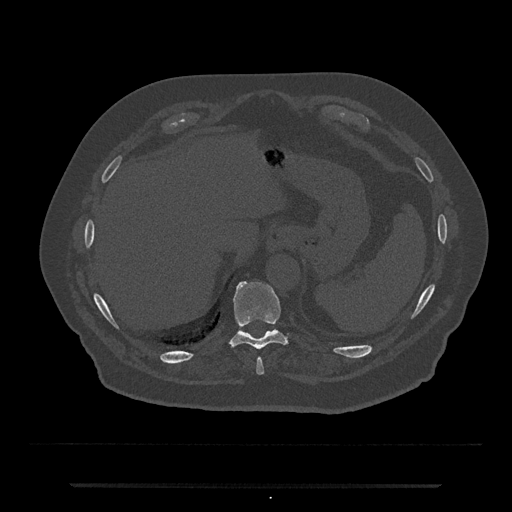
CT including the spine, one axial slice. Slice 706 of 797 in the series (ordered by position). 120 kVp. Bone window (W 1800 / L 400 HU). 0.5 mm slice thickness. 512 × 512 image matrix, field of view 434 × 434 mm. Patient: male, 80 years. Case-level facts recorded for this patient, not image findings: primary cancer: prostate; vertebrae with lytic lesions (as recorded): L1, T11.
Outlined on this slice (semi-automatically segmented with operator editing):
- T10 vertebra: bounding box [x1, y1, x2, y2] px = [231, 281, 287, 350]
- T9 vertebra: [256, 358, 264, 375]